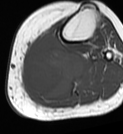
MRI of an extremity soft-tissue mass, one axial slice. MR volume resampled by the dataset authors to the PET/CT grid (not the native acquisition matrix). 3.27 mm slice thickness. 123 × 134 image matrix, field of view 120 × 131 mm. Female patient. Case-level facts recorded for this patient, not image findings: histological type: extraskeletal high grade osteogenic sarcoma; grade: high; site of the primary tumour: left calf.
Annotated regions visible in this slice (expert contour drawn on MRI and transferred to this co-registered scan by the dataset authors):
- gross tumour volume (mass): box from (x=22, y=32) to (x=84, y=99) px